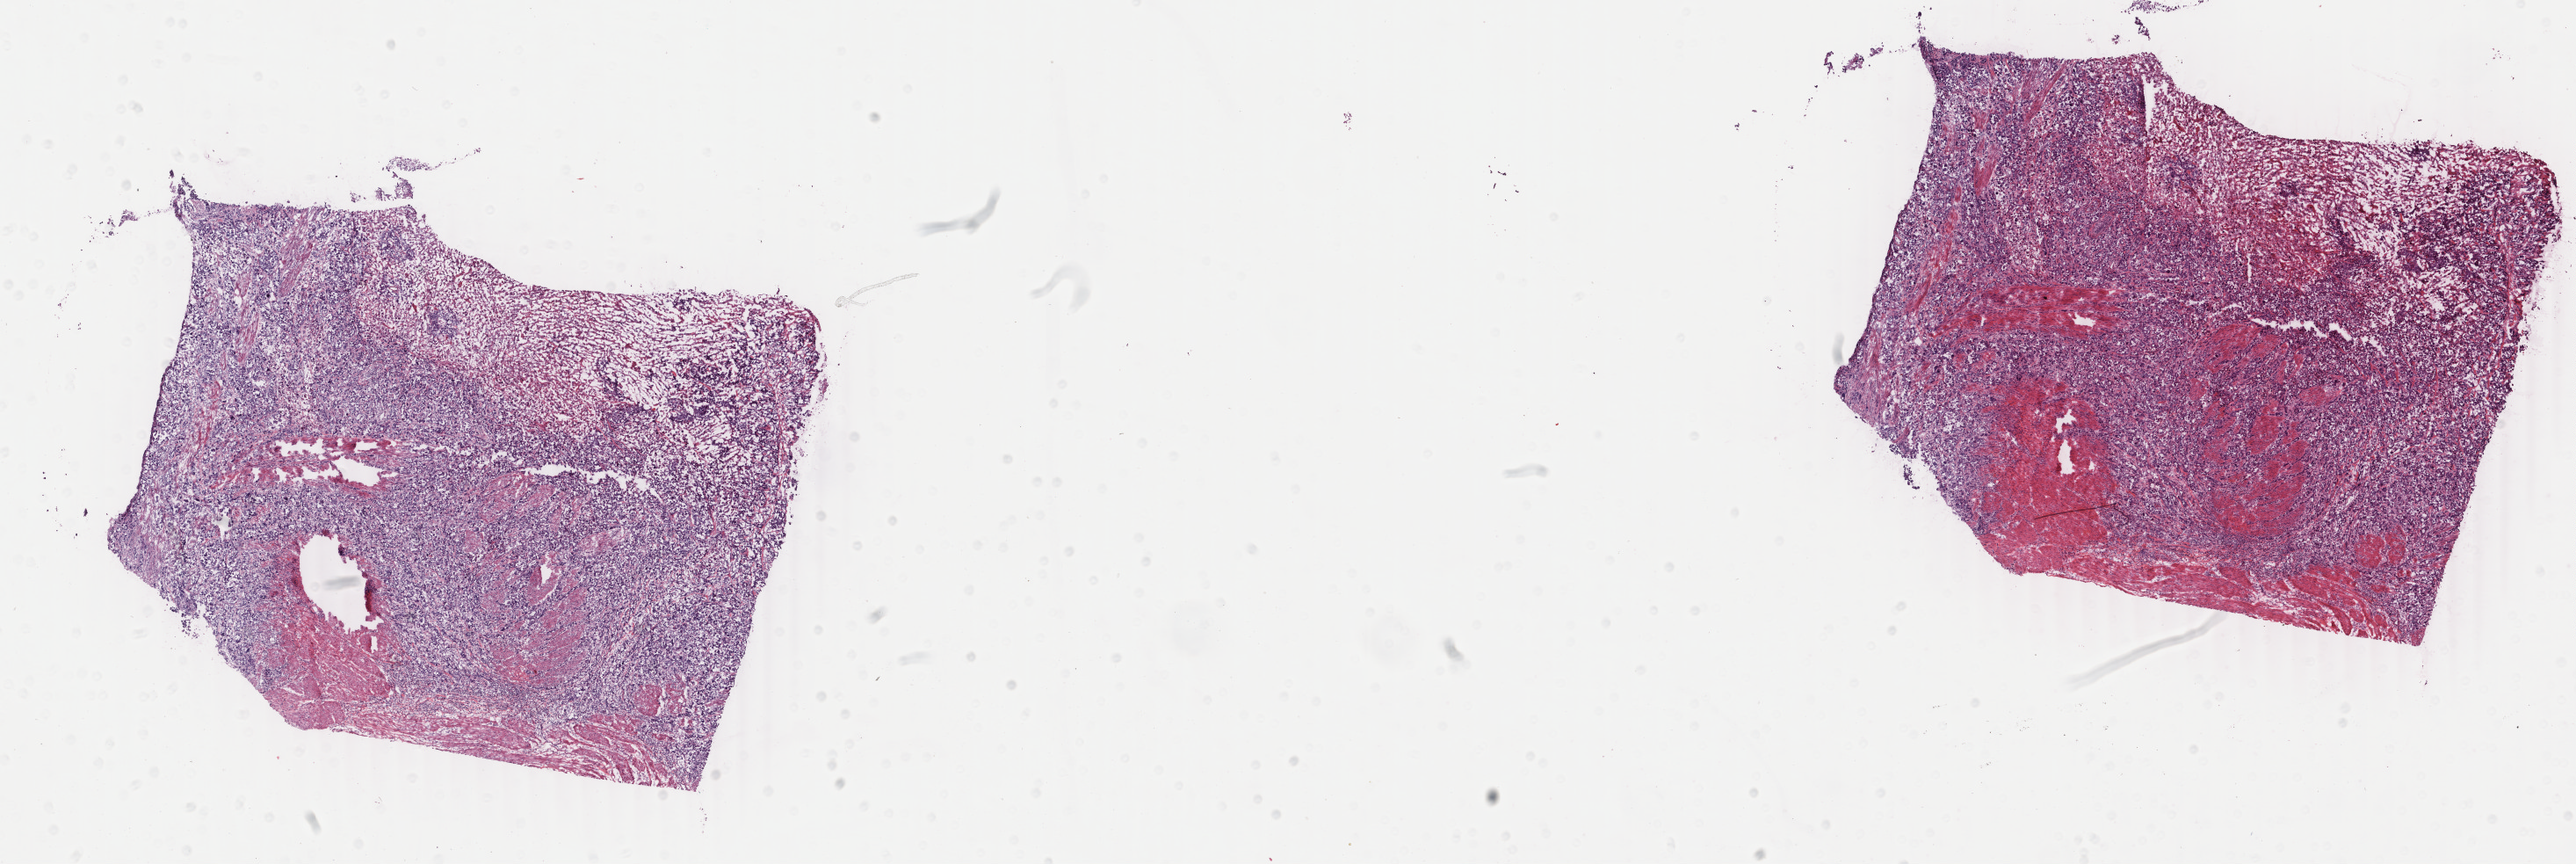
Hematoxylin and eosin (H&E) stained whole-slide image — whole scanned area (about 23.3 x 7.8 mm) shown as a low-resolution overview. Frozen section. Bladder, primary tumour sample. Patient: male, age at initial diagnosis 60 years. Histologic grade: high grade. Pathologist review of this section (percent, as recorded): tumour cells 60%, tumour nuclei 65%, normal cells 20%, stromal cells 0%, necrosis 20%. Infiltration values recorded for this section: lymphocyte infiltration 5%, monocyte infiltration 1%, neutrophil infiltration 15%.
- diagnosis: Transitional cell carcinoma
- AJCC pathologic stage: II (5th edition)
- TNM: T2b N0 M0